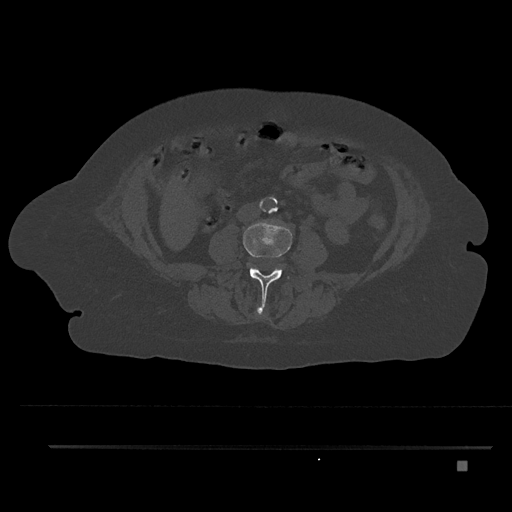
CT including the spine, one axial slice. Slice 120 of 797 in the series (ordered by position). Reconstruction kernel Br40s/3. Bone window (W 1800 / L 400 HU). 0.5 mm slice thickness. 512 × 512 image matrix, field of view 437 × 437 mm. Patient: female, 76 years. From the clinical record (not read from this slice): primary cancer: lung; vertebrae with lytic lesions (as recorded): T11, L3.
Outlined on this slice (semi-automatic segmentation, software-assisted and operator-edited):
- L2 vertebra: bounding box (x1, y1, x2, y2) in pixels: (256, 306, 264, 317)
- L3 vertebra: (243, 220, 292, 307)